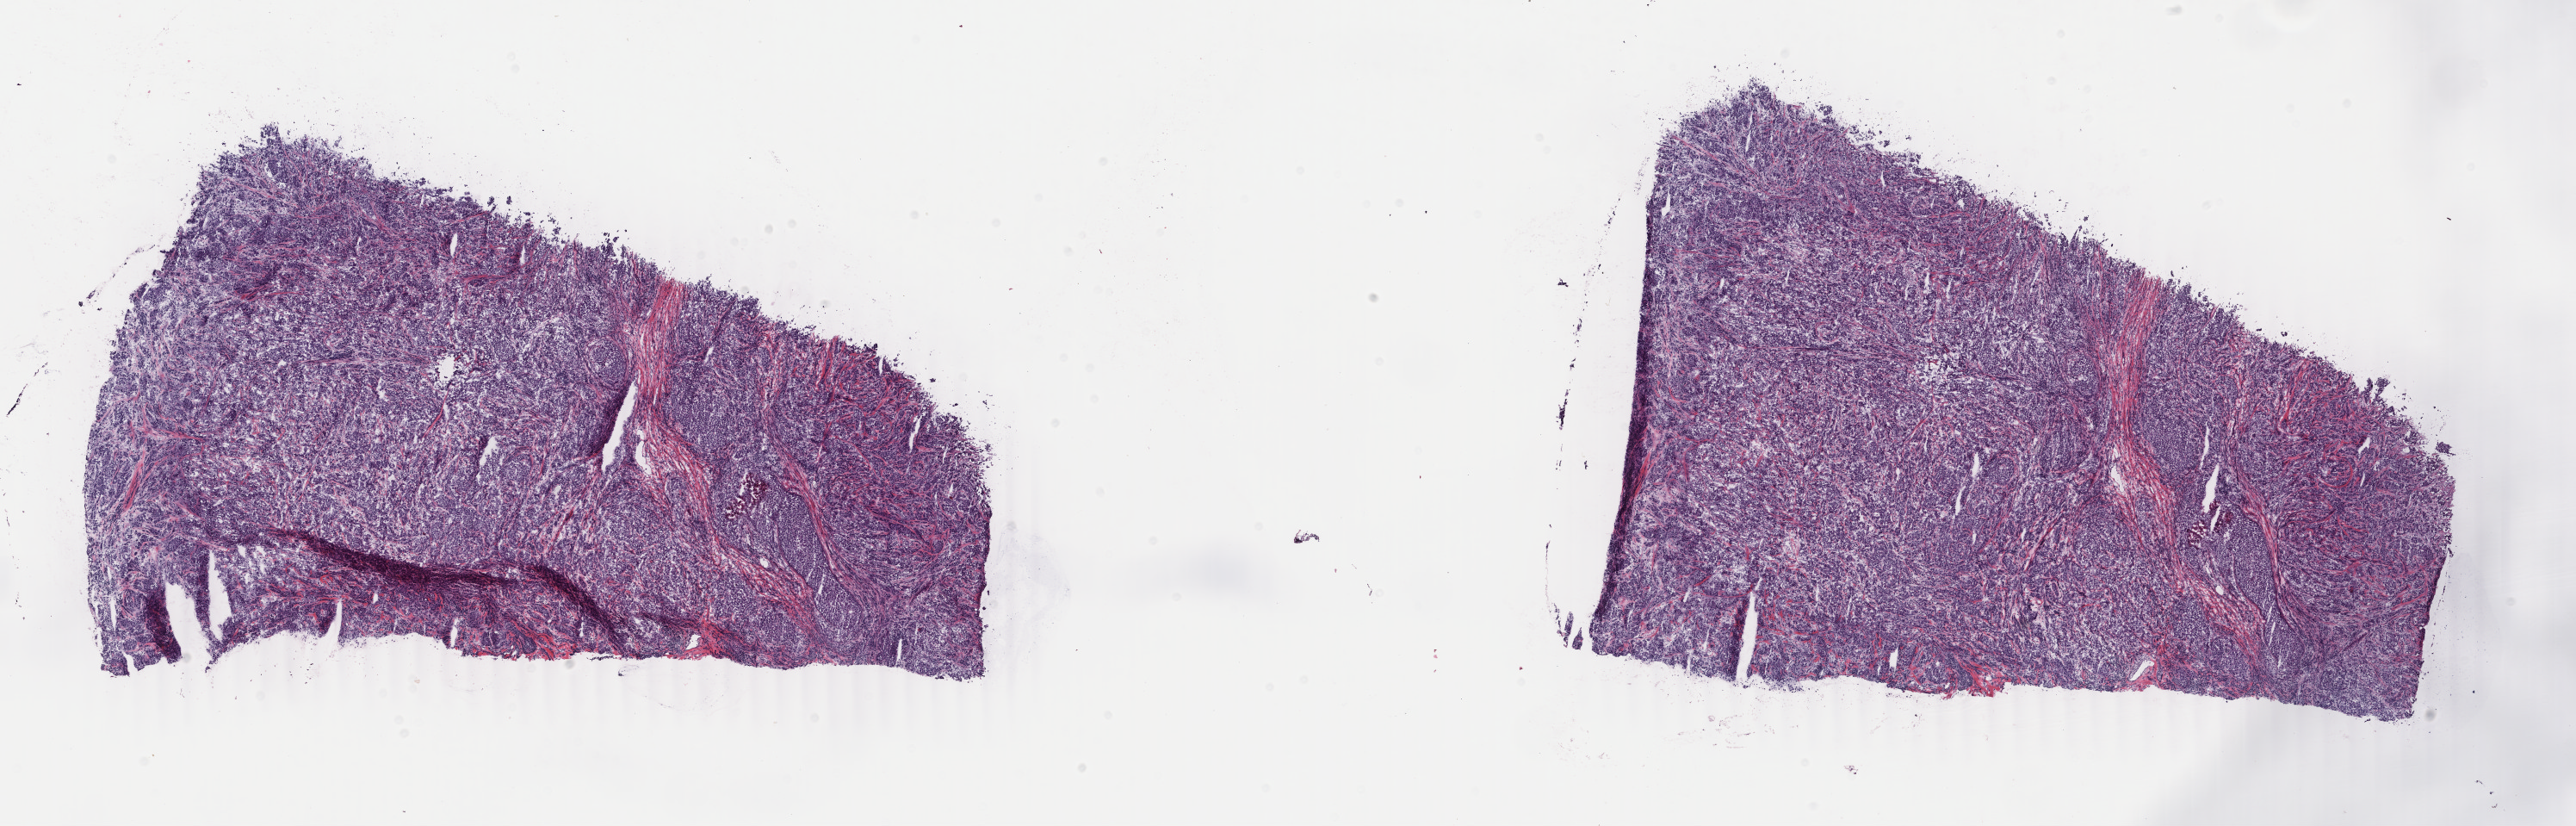
Hematoxylin and eosin (H&E) stained whole-slide image — shown as a low-resolution overview of the whole scanned area (about 23.8 x 7.6 mm, from a 40x scan). Frozen section from the top of the tissue portion. Breast, primary tumour sample. Patient: female, age at initial diagnosis 50 years. Pathologist review of this section (percent, as recorded): tumour cells 90%, tumour nuclei 90%, normal cells 0%, stromal cells 9%, necrosis 1%. Inflammatory infiltration, as recorded: lymphocyte infiltration 2%, monocyte infiltration 0%, neutrophil infiltration 0%.
- AJCC pathologic stage: IIIA
- TNM: T3 N1 M0
- histologic diagnosis: Infiltrating duct carcinoma, NOS
- lymph nodes positive (case pathology): 3 of 27 examined